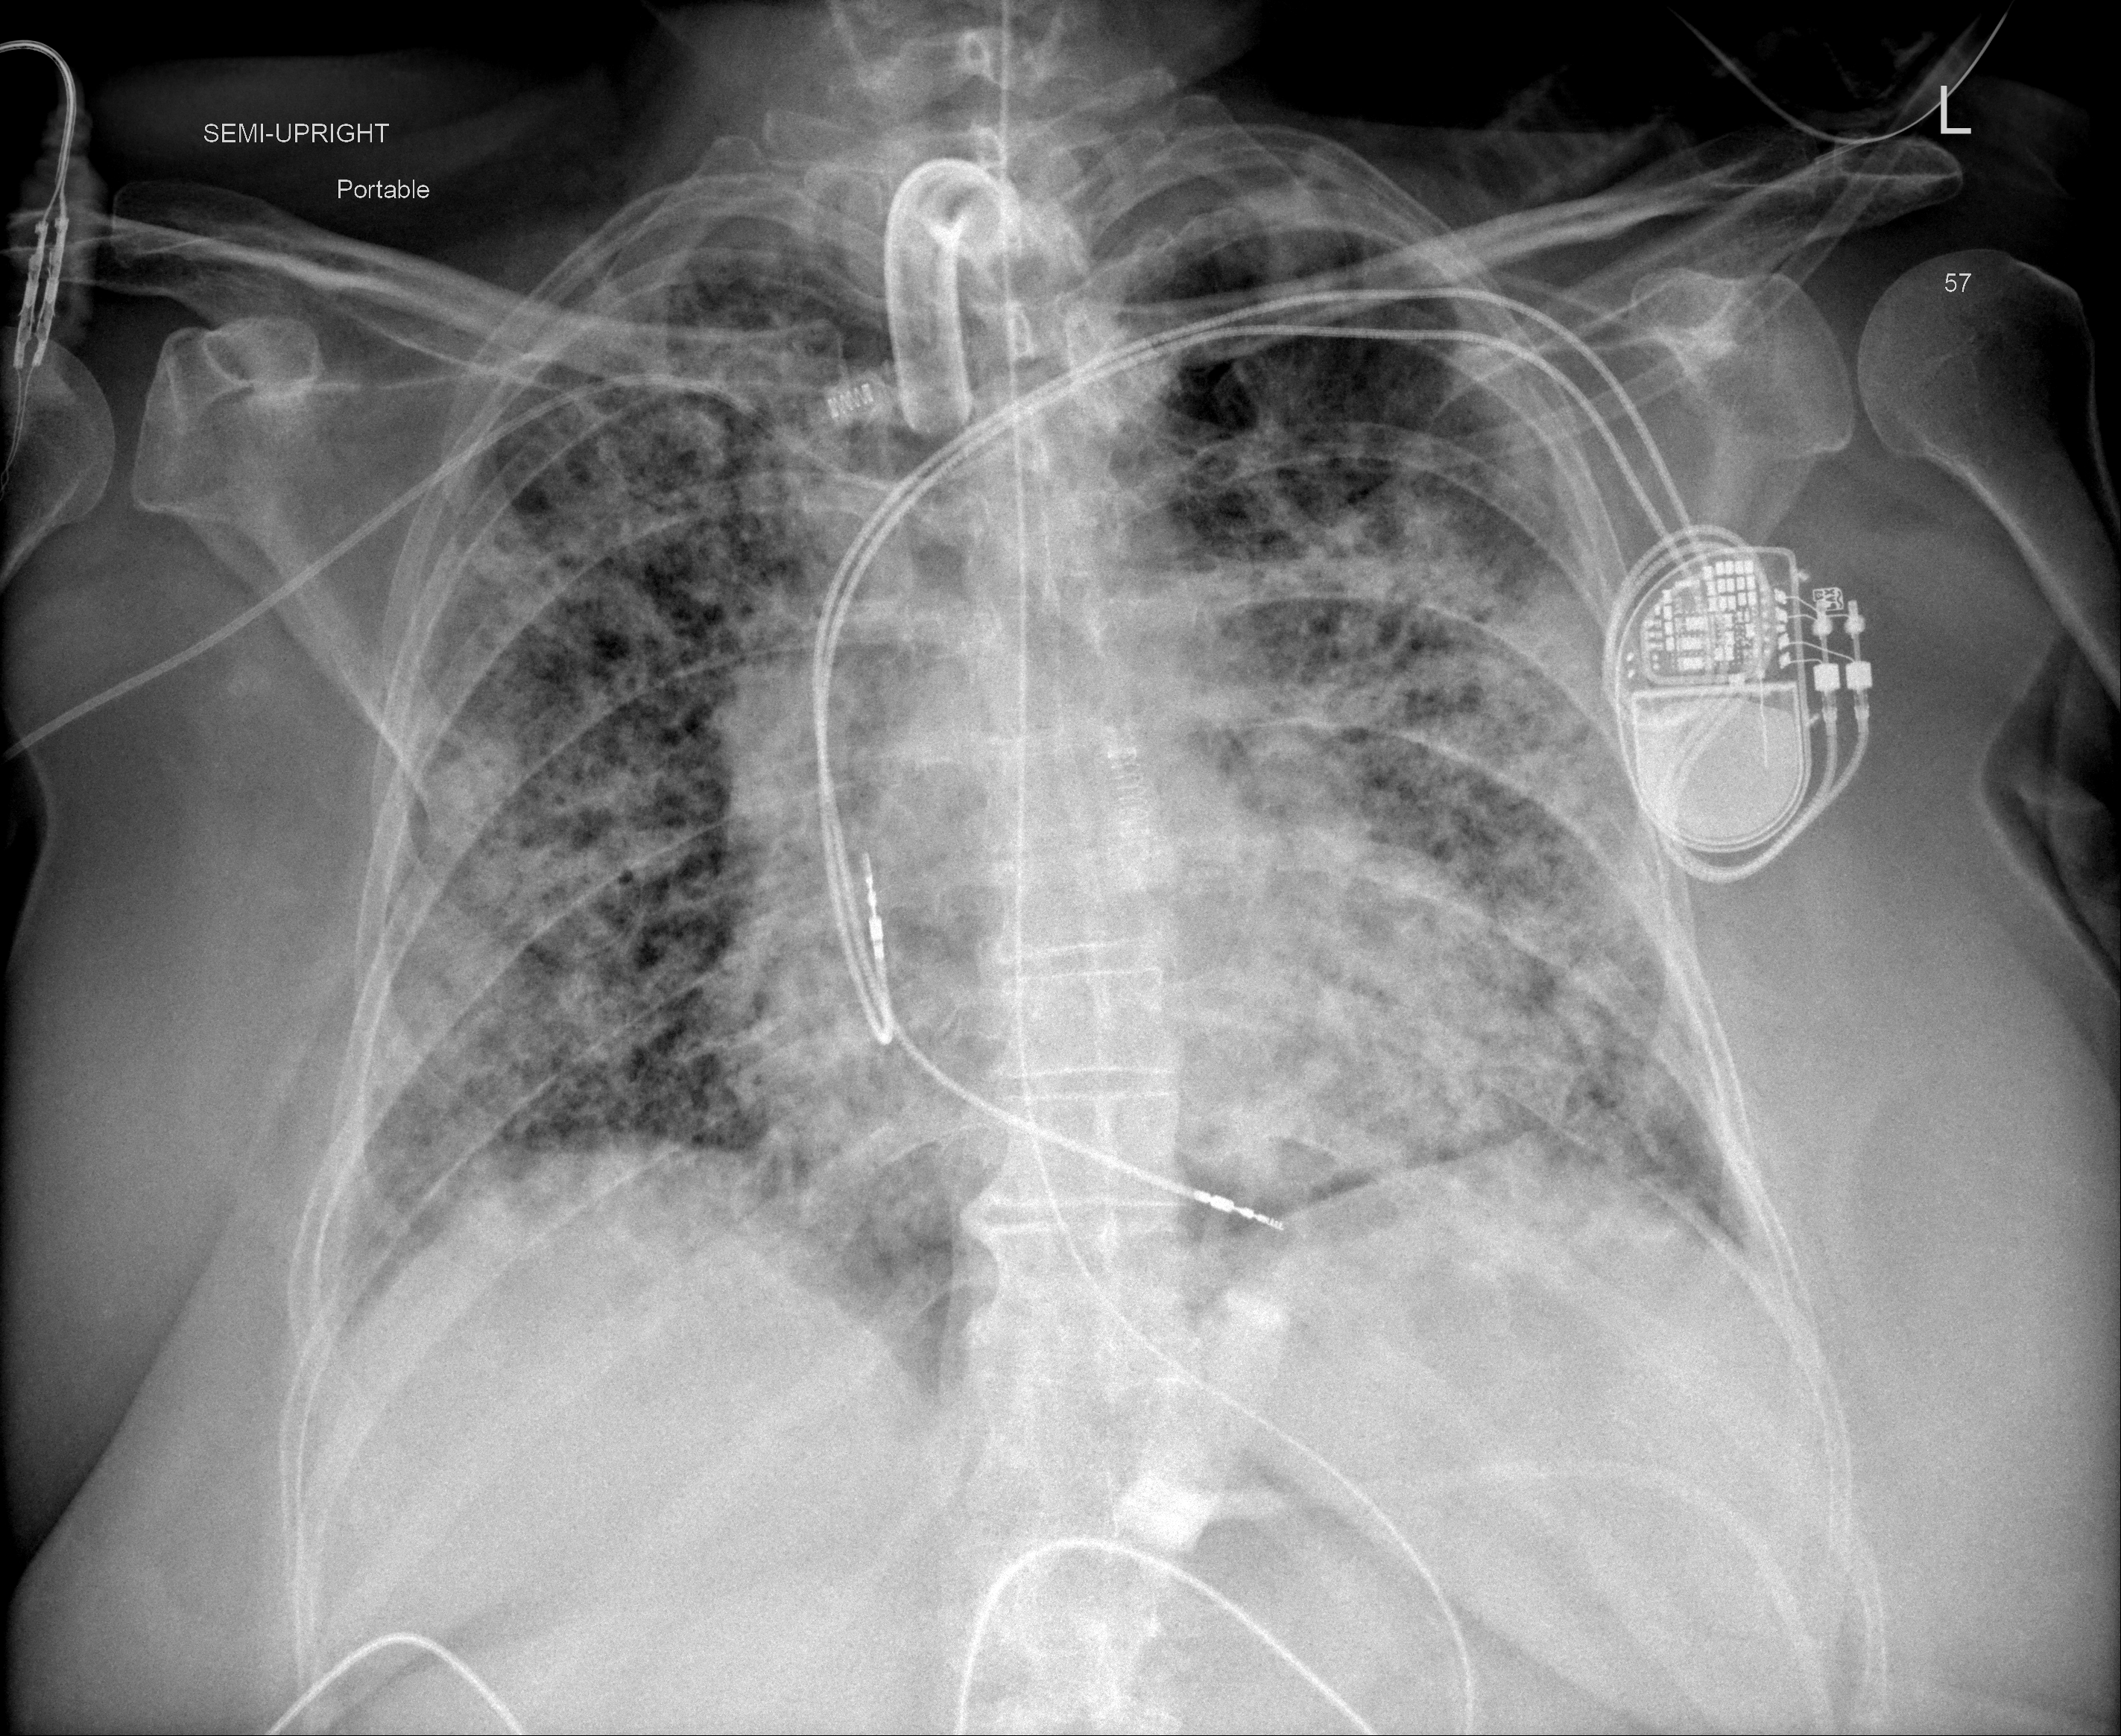
Chest X-ray (portable), AP projection. Female patient, age 57 years; imaged 26 days after the COVID-19 diagnosis.
Key findings recorded by the radiologist: Largely unchanged extensive bilateral airspace opacities.